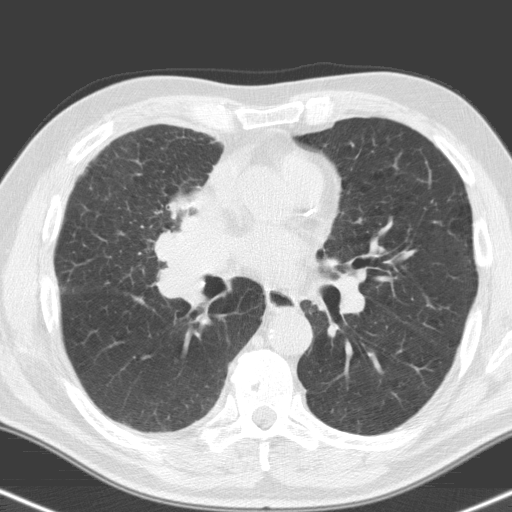
Low-dose screening chest CT, one axial slice; position 86 of 160 along the scan axis; 120 kVp; lung window (W 1500 / L -600 HU); 3.2 mm slice thickness; 512 × 512 image matrix.
Annotated regions visible in this slice (expert manual segmentation):
- lesion 1 (tumor, hilum of right lung): bounding box (x1, y1, x2, y2) in pixels: (156, 184, 244, 305)